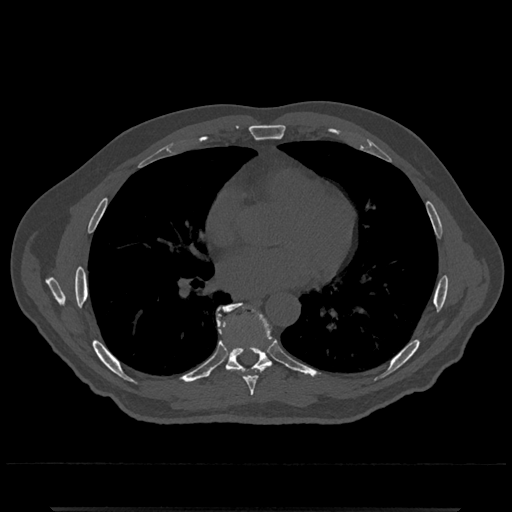
CT including the spine, one axial slice; slice 695 of 797 in the series (ordered by position); bone window (W 1800 / L 400 HU); 0.5 mm slice thickness; 512 × 512 image matrix, field of view 393 × 393 mm. Patient: male, 67 years. From the clinical record (not read from this slice): primary cancer: prostate.
Structures marked on this image (semi-automatic segmentation, software-assisted and operator-edited):
- T7 vertebra: bounding box (x1, y1, x2, y2) in pixels: (218, 322, 271, 396)
- T8 vertebra: (216, 302, 271, 373)